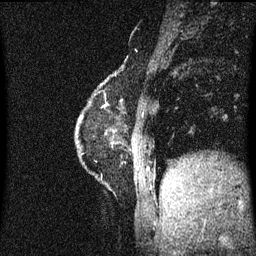
Breast MRI (dynamic contrast-enhanced), one sagittal slice; position 13 of 60 along the scan axis; dynamic contrast-enhanced series, image 2 of 3 at this slice position (ordered by acquisition); 1.5 T; TE 4.2 ms, TR 8.4 ms; 256 × 256 image matrix, field of view 200 × 200 mm. Female patient, age 60 years.
Annotated regions visible in this slice (semi-automatically segmented with operator editing):
- analysis volume of interest (the breast-tissue region the enhancement analysis was run in; not a lesion): box from (x=73, y=76) to (x=125, y=191) px
- tumour enhancement mask (voxels above the 70 % enhancement threshold inside the analysis volume of interest): (x=81, y=84)–(x=102, y=119)